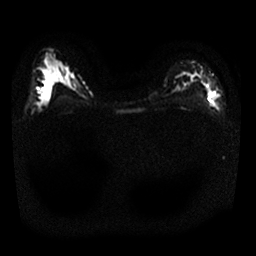
Breast MRI, one axial slice. Slice 19 of 25 in the series (ordered by position). Diffusion-weighted series; image 2 of 4 stored at this slice position (different b-values; order by instance number). 1.5 T. 256 × 256 image matrix, field of view 320 × 320 mm. Female patient.
Structures marked on this image (manually delineated by an expert):
- tumour on diffusion-weighted imaging: bounding box <208,92,214,96> (left, top, right, bottom; pixels)